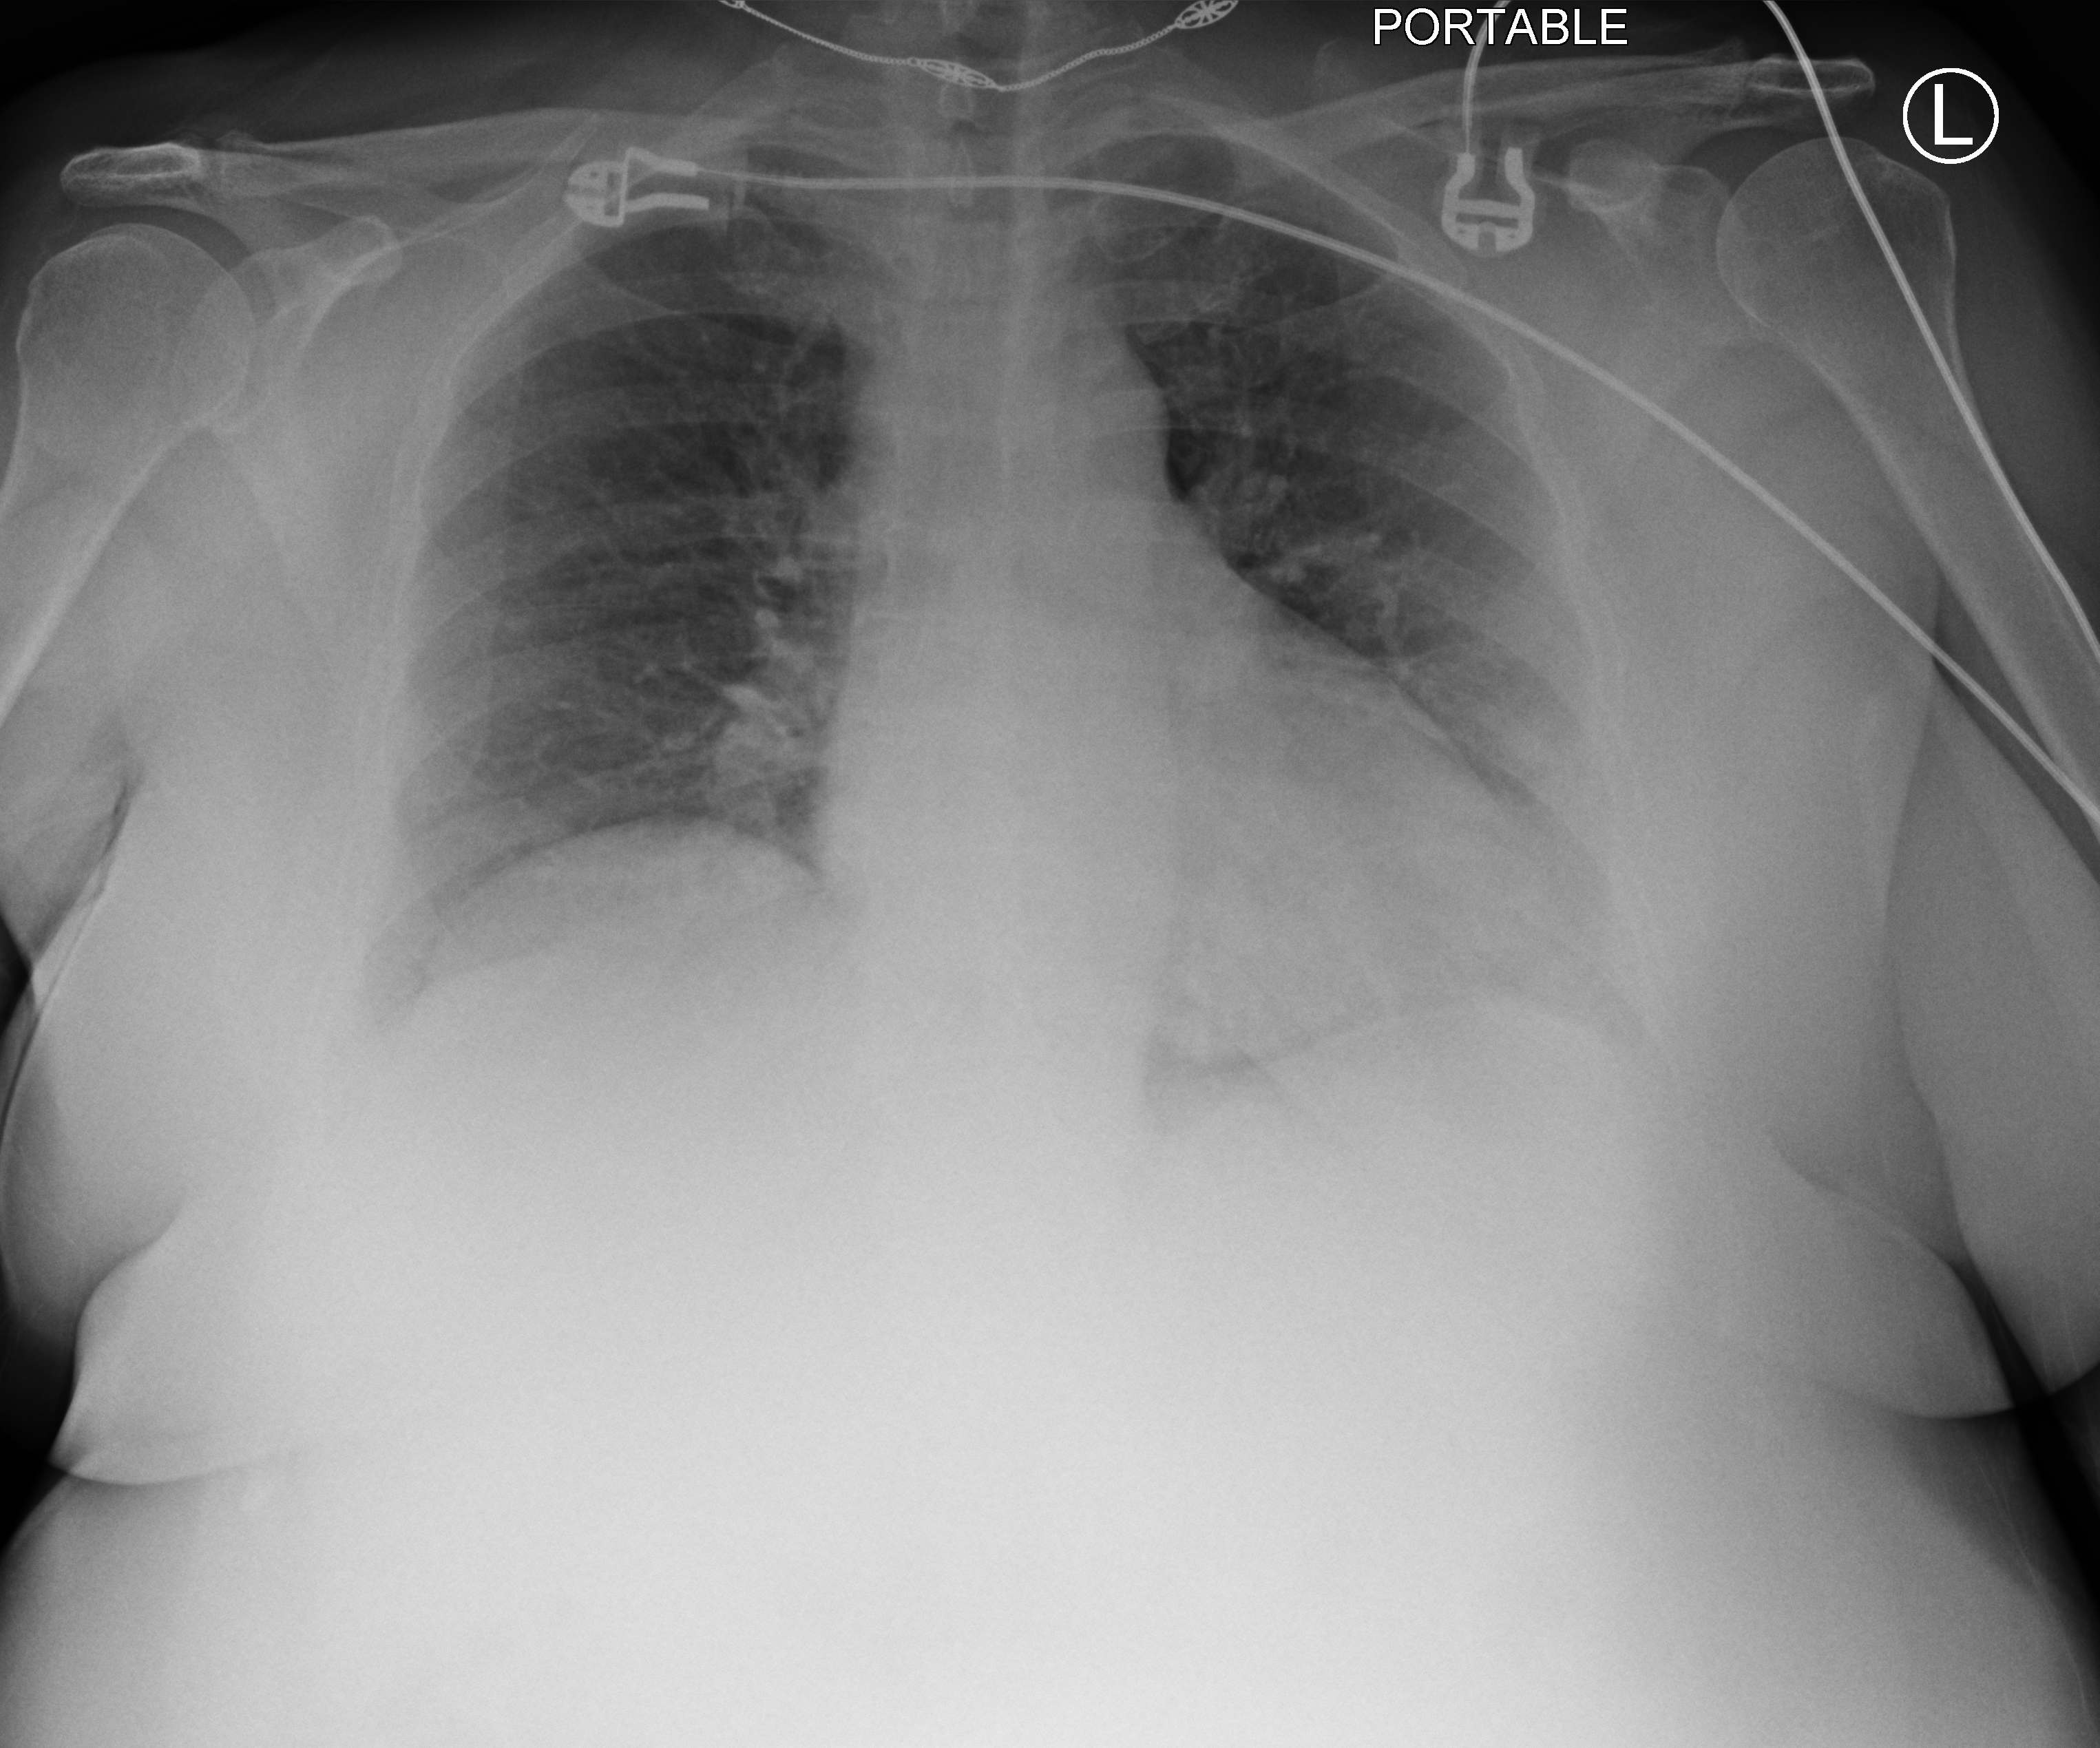
Portable chest radiograph. Patient hospitalised with COVID-19, aged 60–74 years.
Hospital-stay facts (about this admission, not read from this image; timing relative to this image not recorded):
- admitted to intensive care during this hospital stay: no